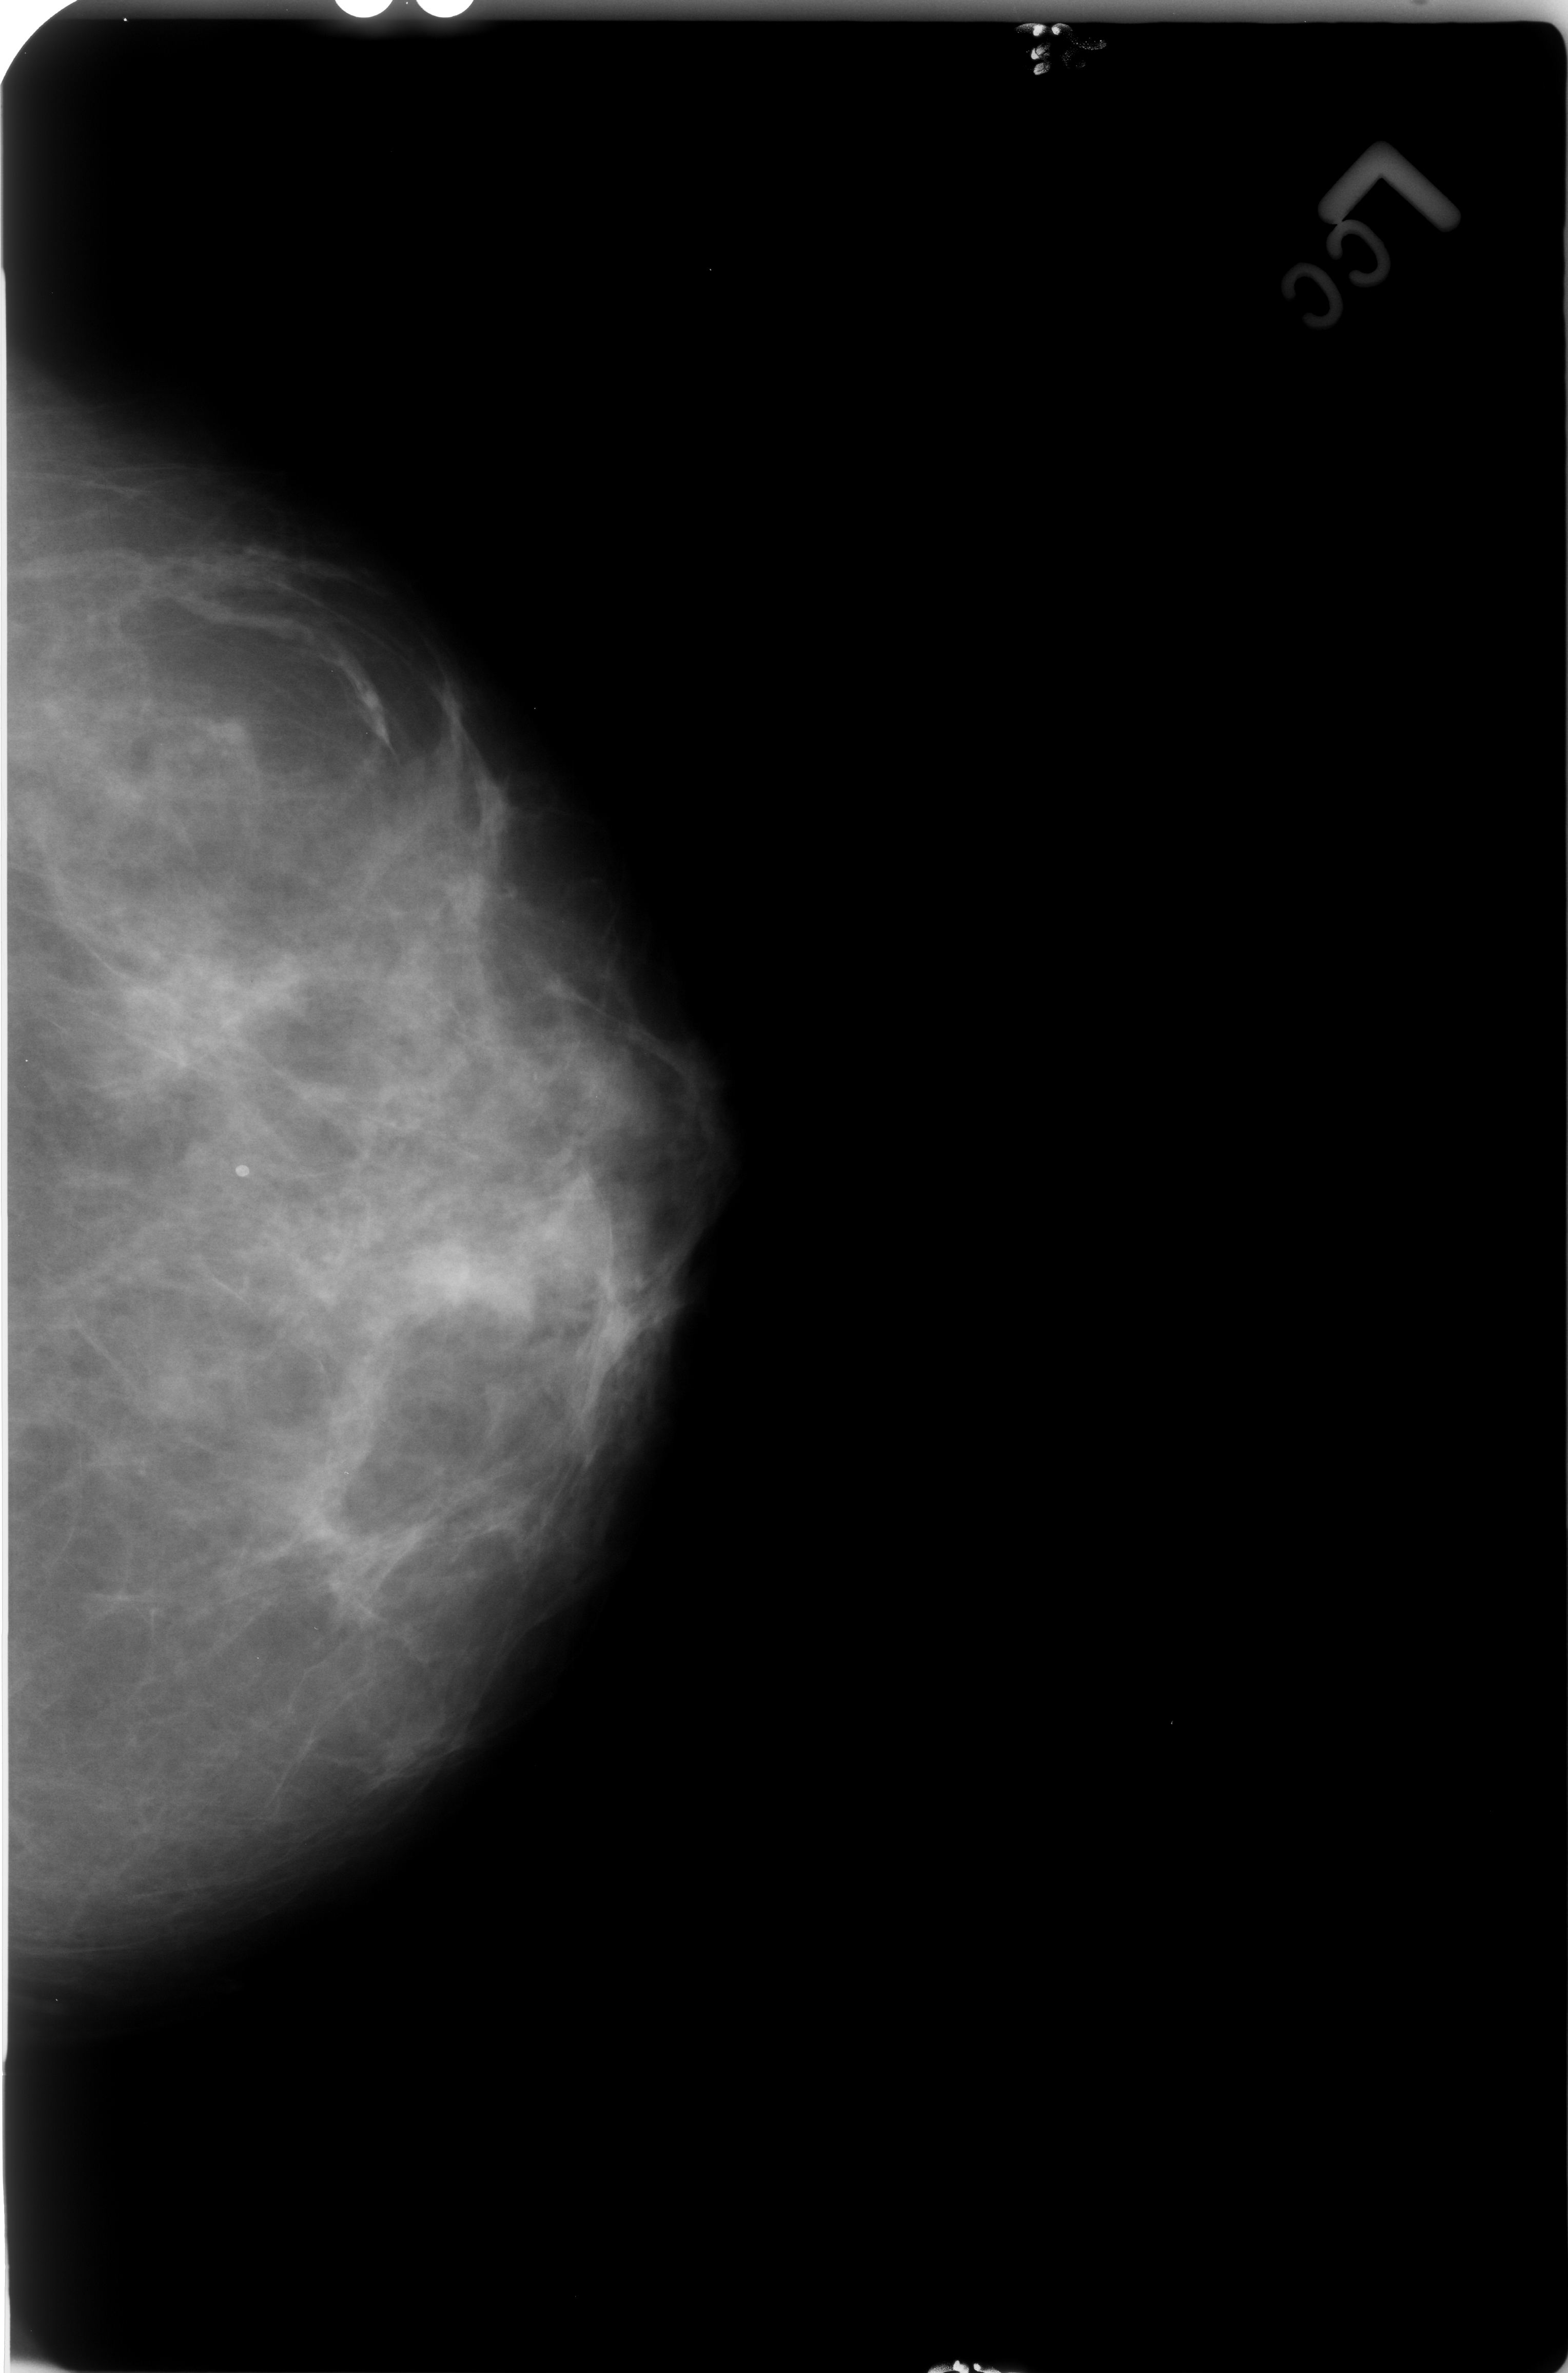
Digitized screen-film mammogram, left breast, craniocaudal (CC) view, BI-RADS breast density category 3 (scale 1–4).
Calcifications, morphology lucent center; BI-RADS assessment category 2; benign; no additional work-up was recommended (benign without callback).